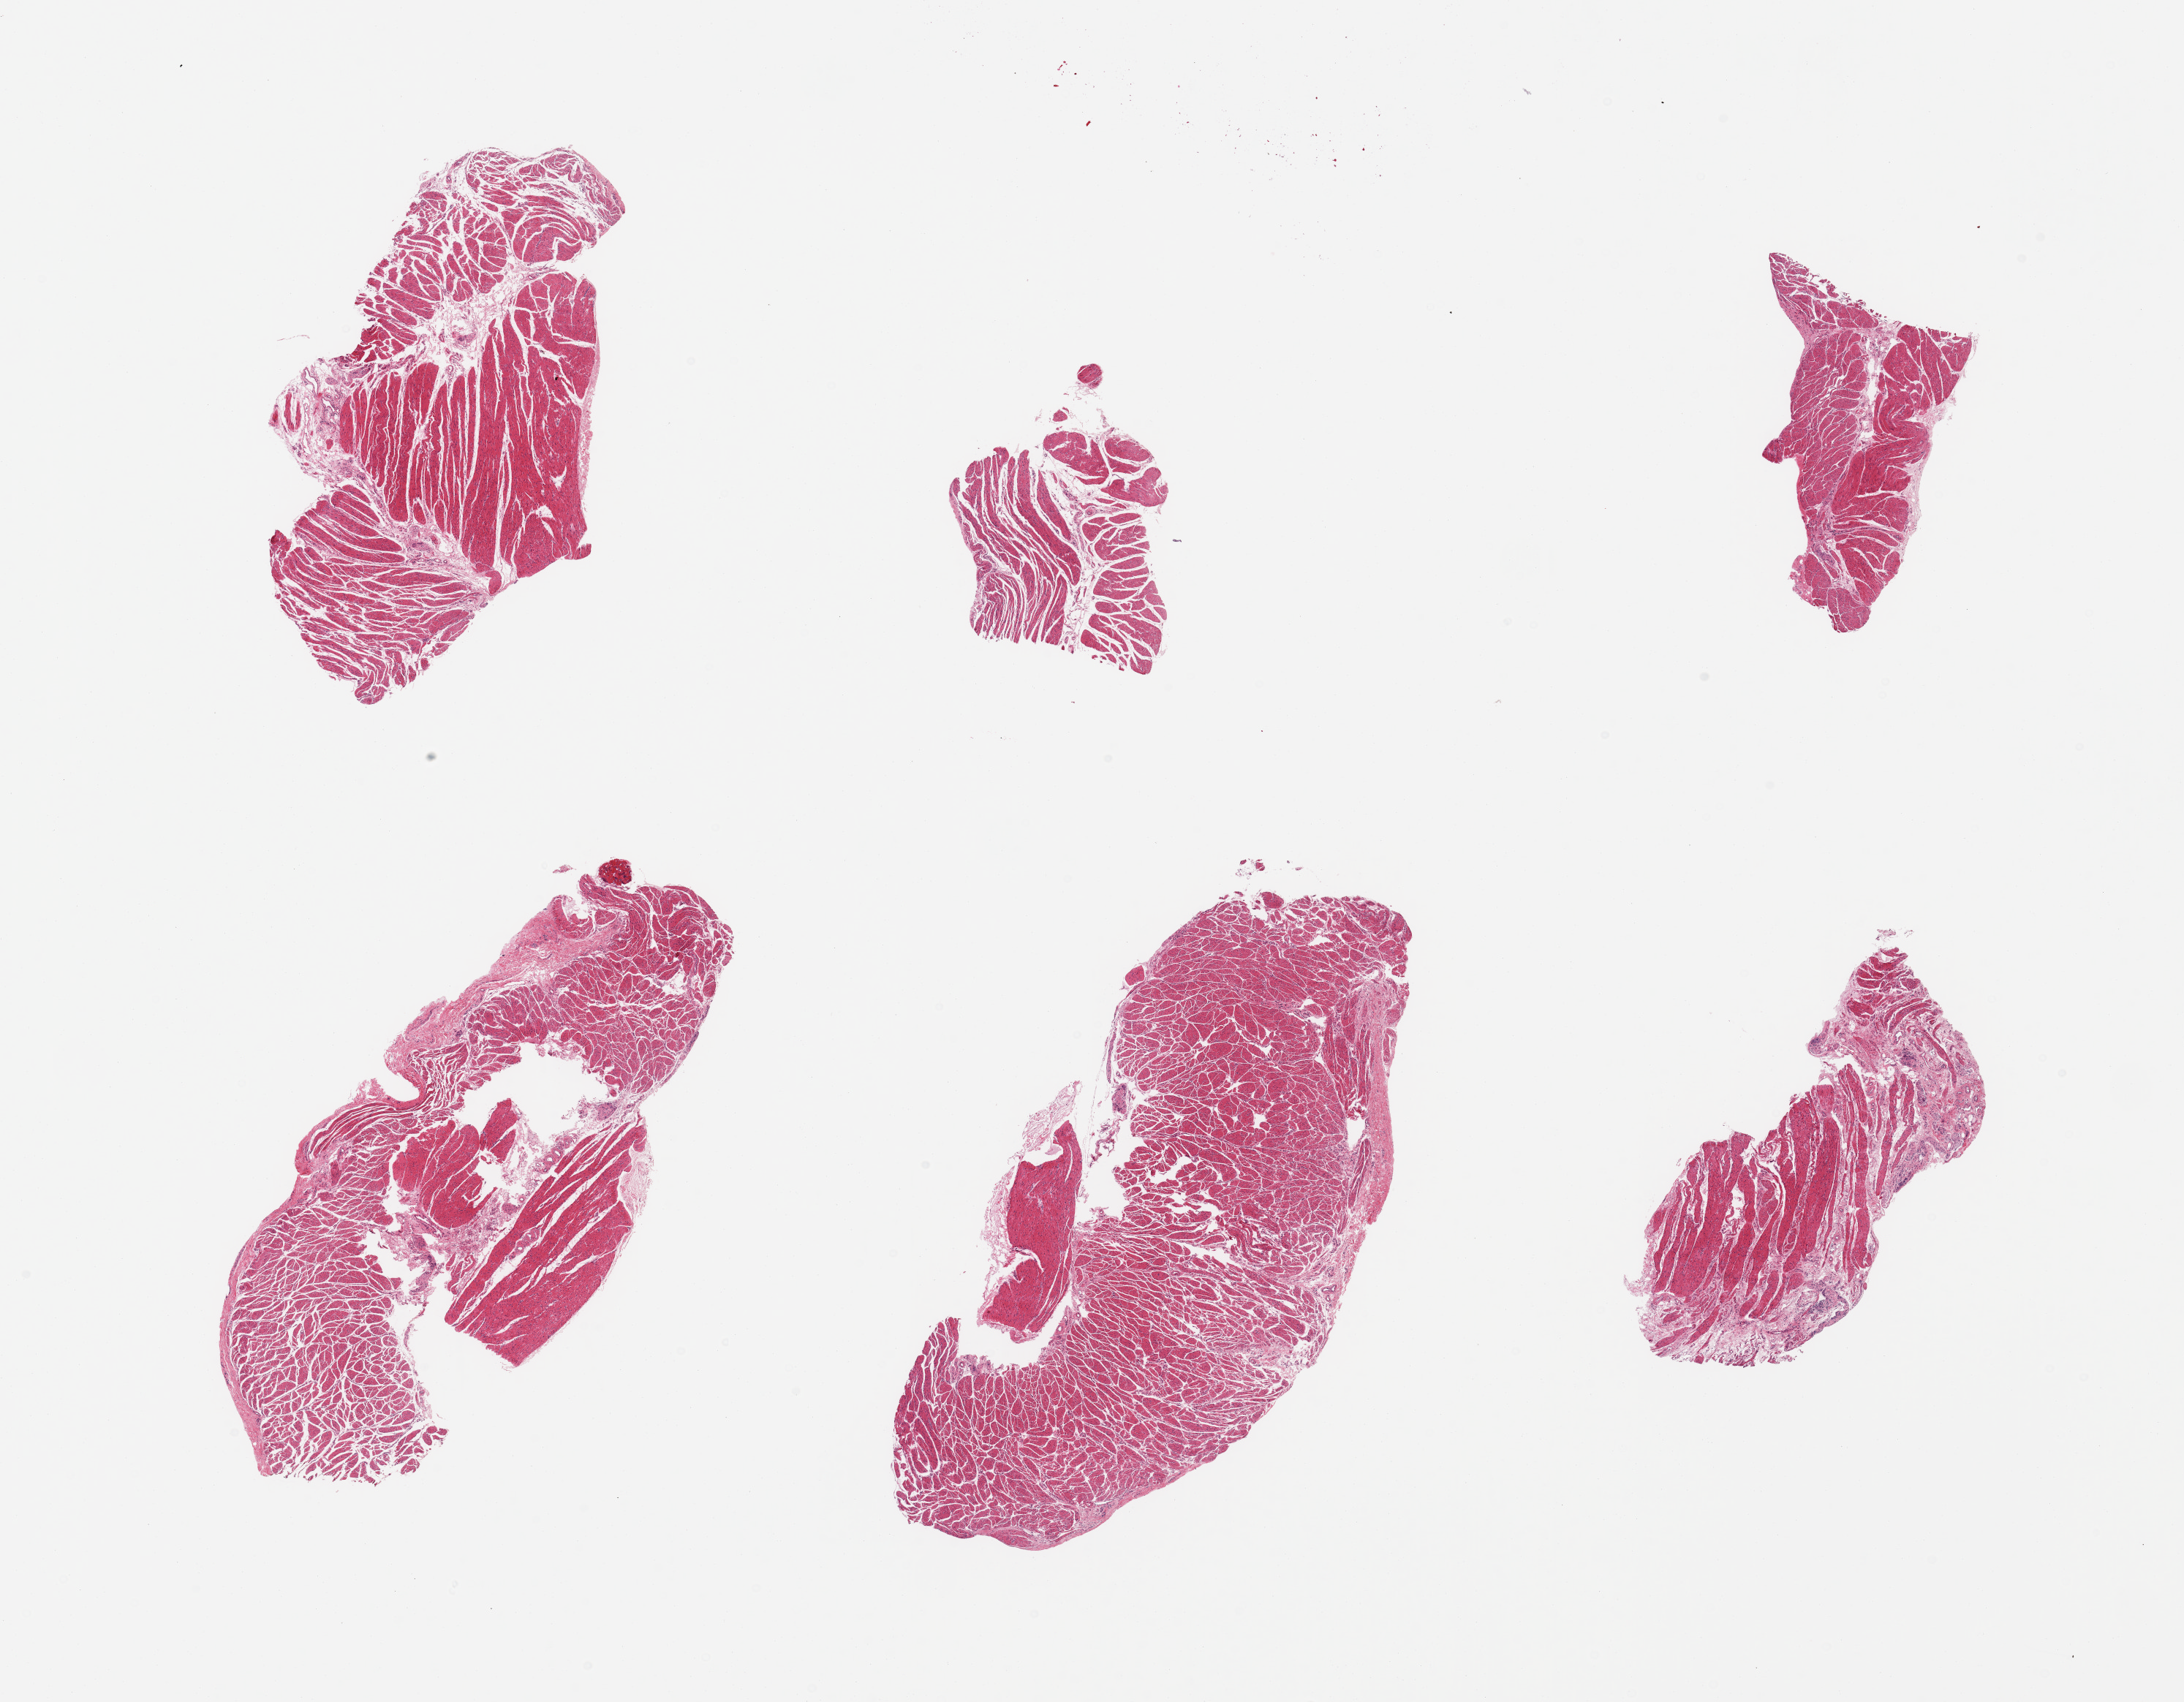
Digitized haematoxylin and eosin-stained section, whole scanned area (about 23.6 x 18.4 mm) shown as a low-resolution overview; PAXgene-fixed paraffin-embedded (PFPE) section; section of esophageal muscle (target tissue); tissue donor sample. Donor: male.
* review note (as recorded): 6 pieces; target muscularis